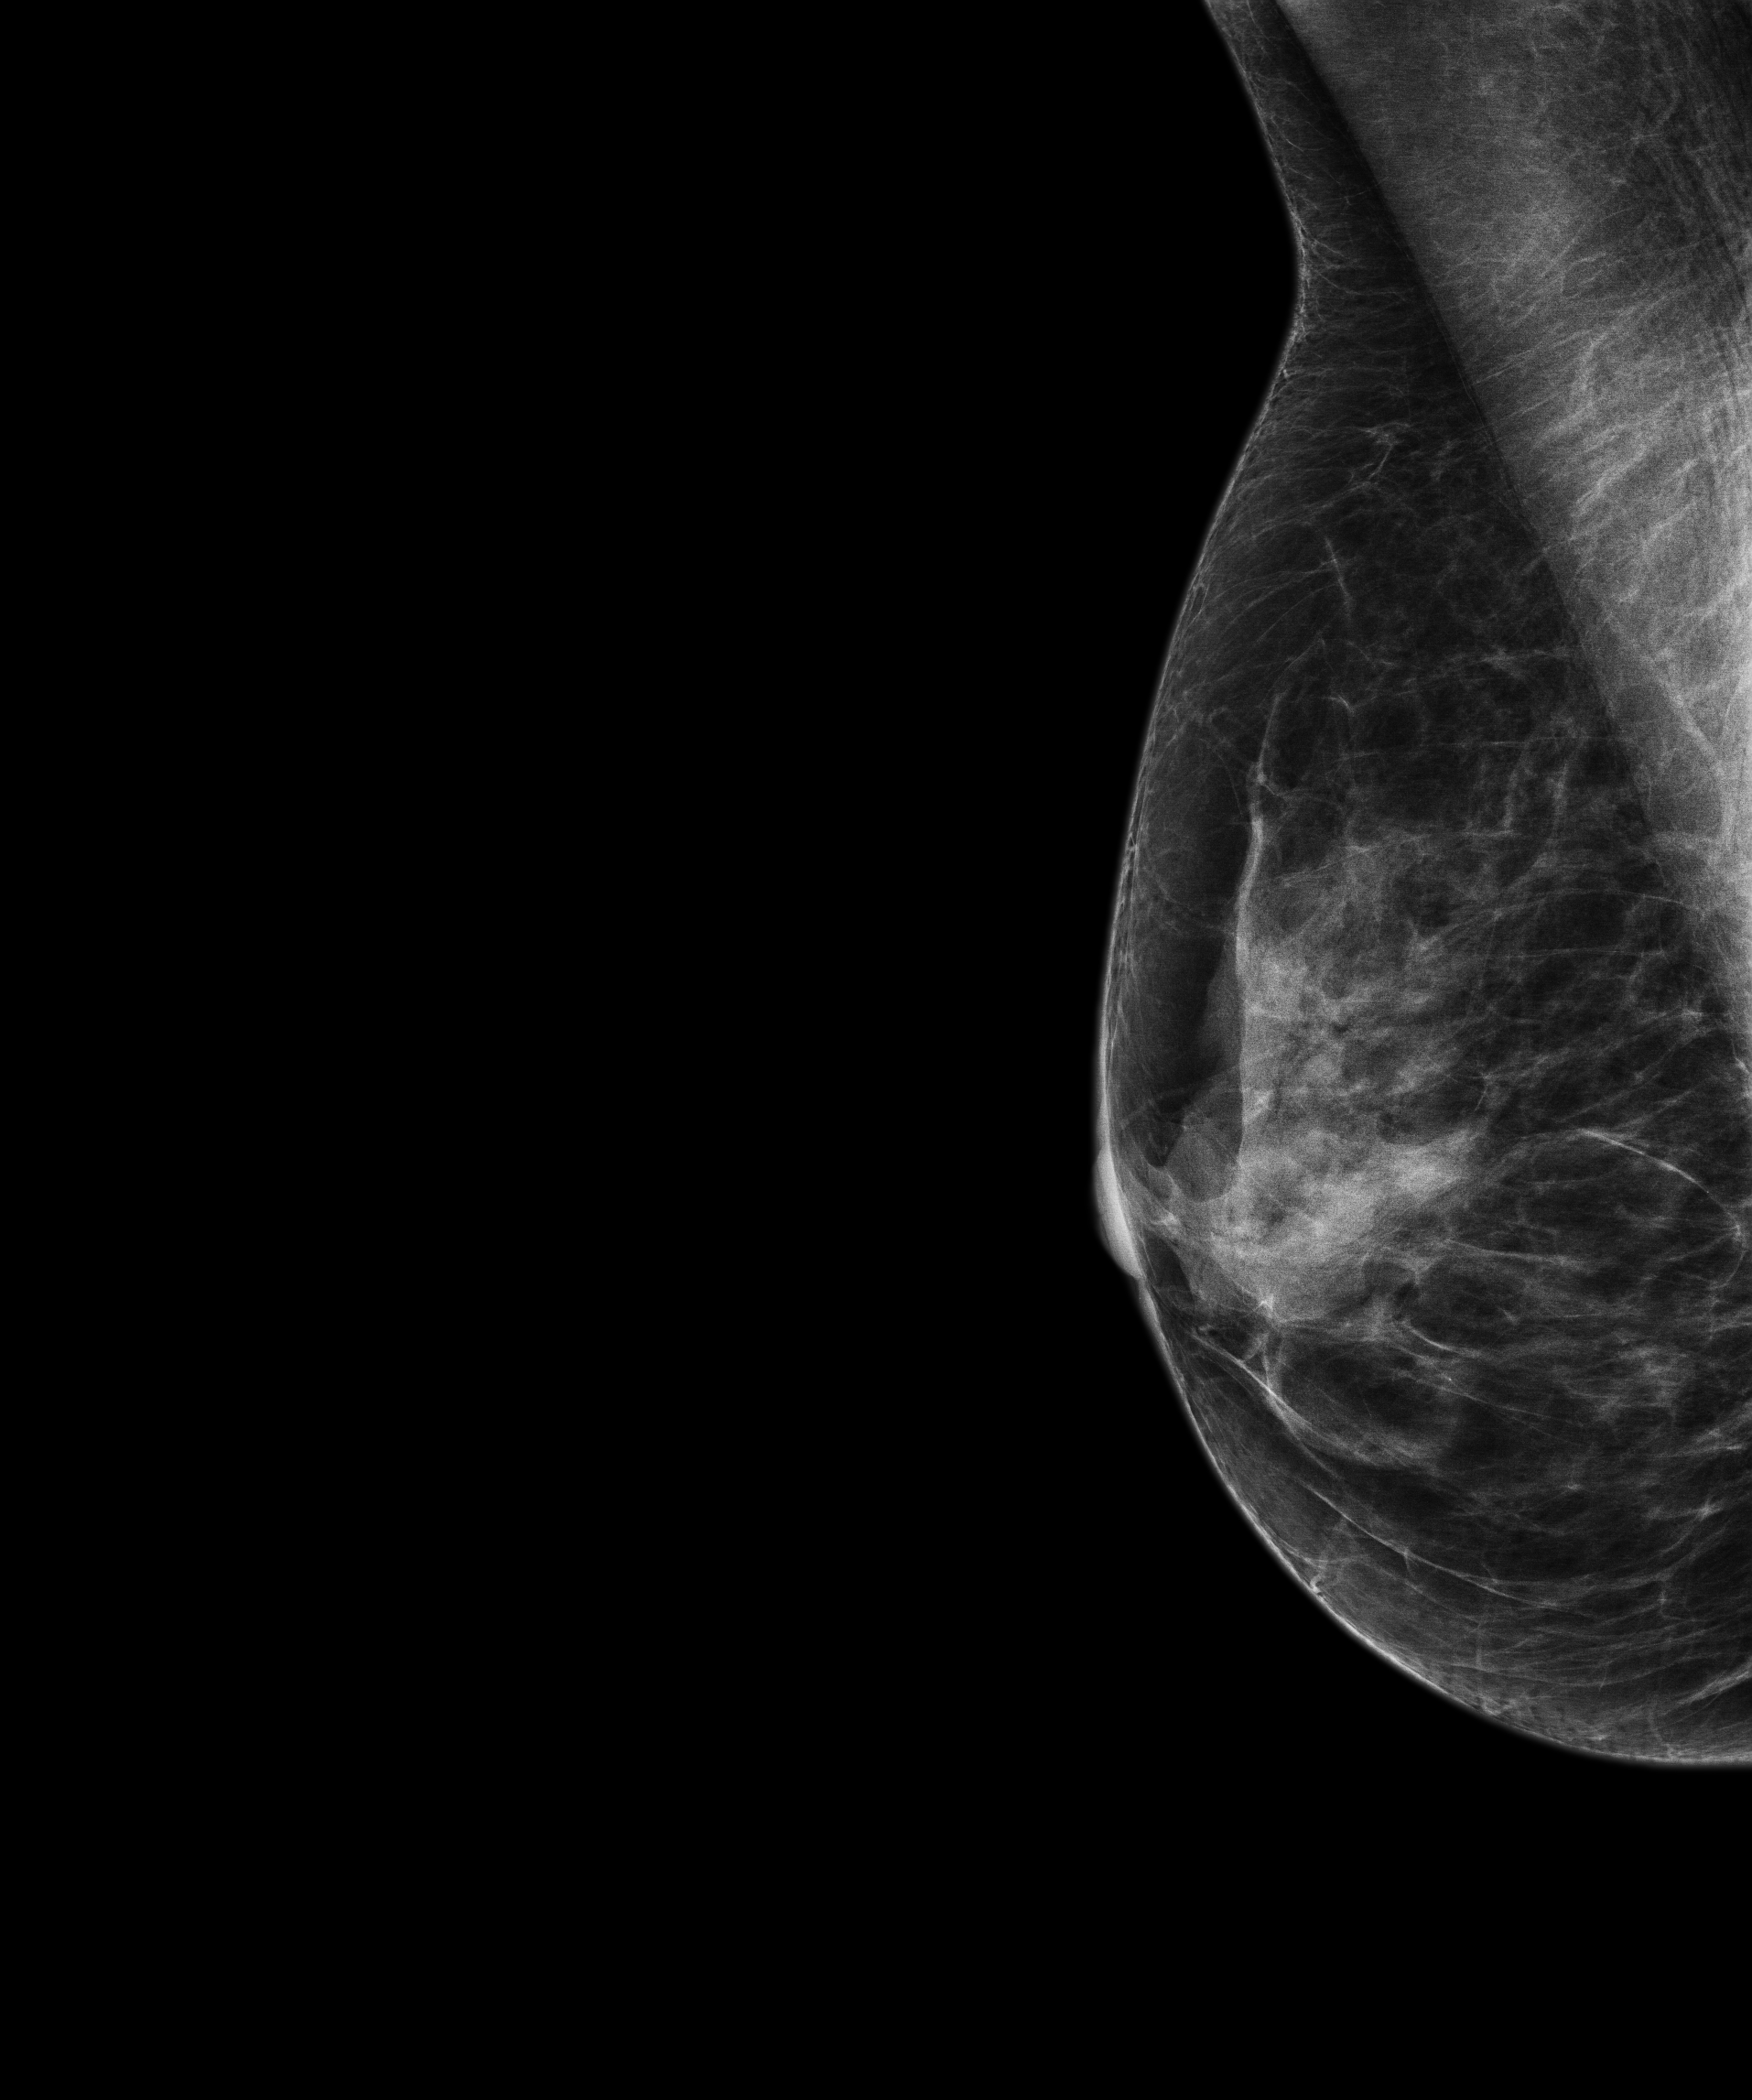
Screening examination; system: Senographe Pristina. Female patient, age 66 years.
Image type: full-field digital mammogram. Breast: right. Projection: MLO view.